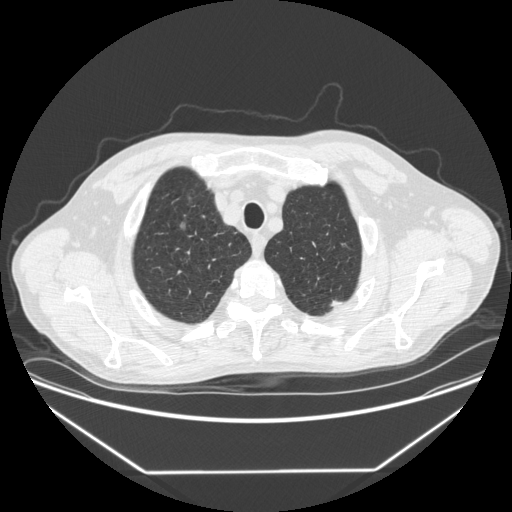
Low-dose screening chest CT, one axial slice; position 337 of 383 along the scan axis; reconstruction kernel STANDARD; 120 kVp; lung window (W 1500 / L -600 HU); 1.25 mm slice thickness; 512 × 512 image matrix, field of view 418 × 418 mm.
Annotated regions visible in this slice (outlined manually by an expert reader):
- lesion 1 (tumor, upper lobe of left lung): bounding box <330,300,342,307> (left, top, right, bottom; pixels)